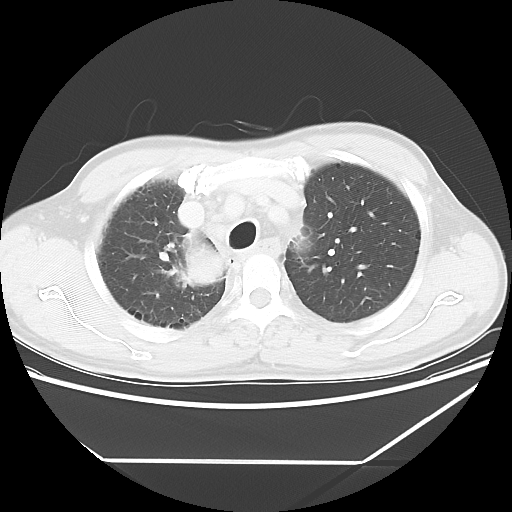
Chest CT, one axial slice. Slice 47 of 60 in the series (ordered by position). Reconstruction kernel LUNG. Lung window (W 1500 / L -600 HU). 5 mm slice thickness. 512 × 512 image matrix. Male patient, age 58 years. Case-level facts recorded for this patient, not image findings: clinical TNM (as recorded): T2 N2 M0.
Annotated regions visible in this slice (rectangle marked by the reading radiologist):
- lung tumour (recorded histology: squamous cell carcinoma): bounding box (x1, y1, x2, y2) in pixels: (170, 240, 229, 300)